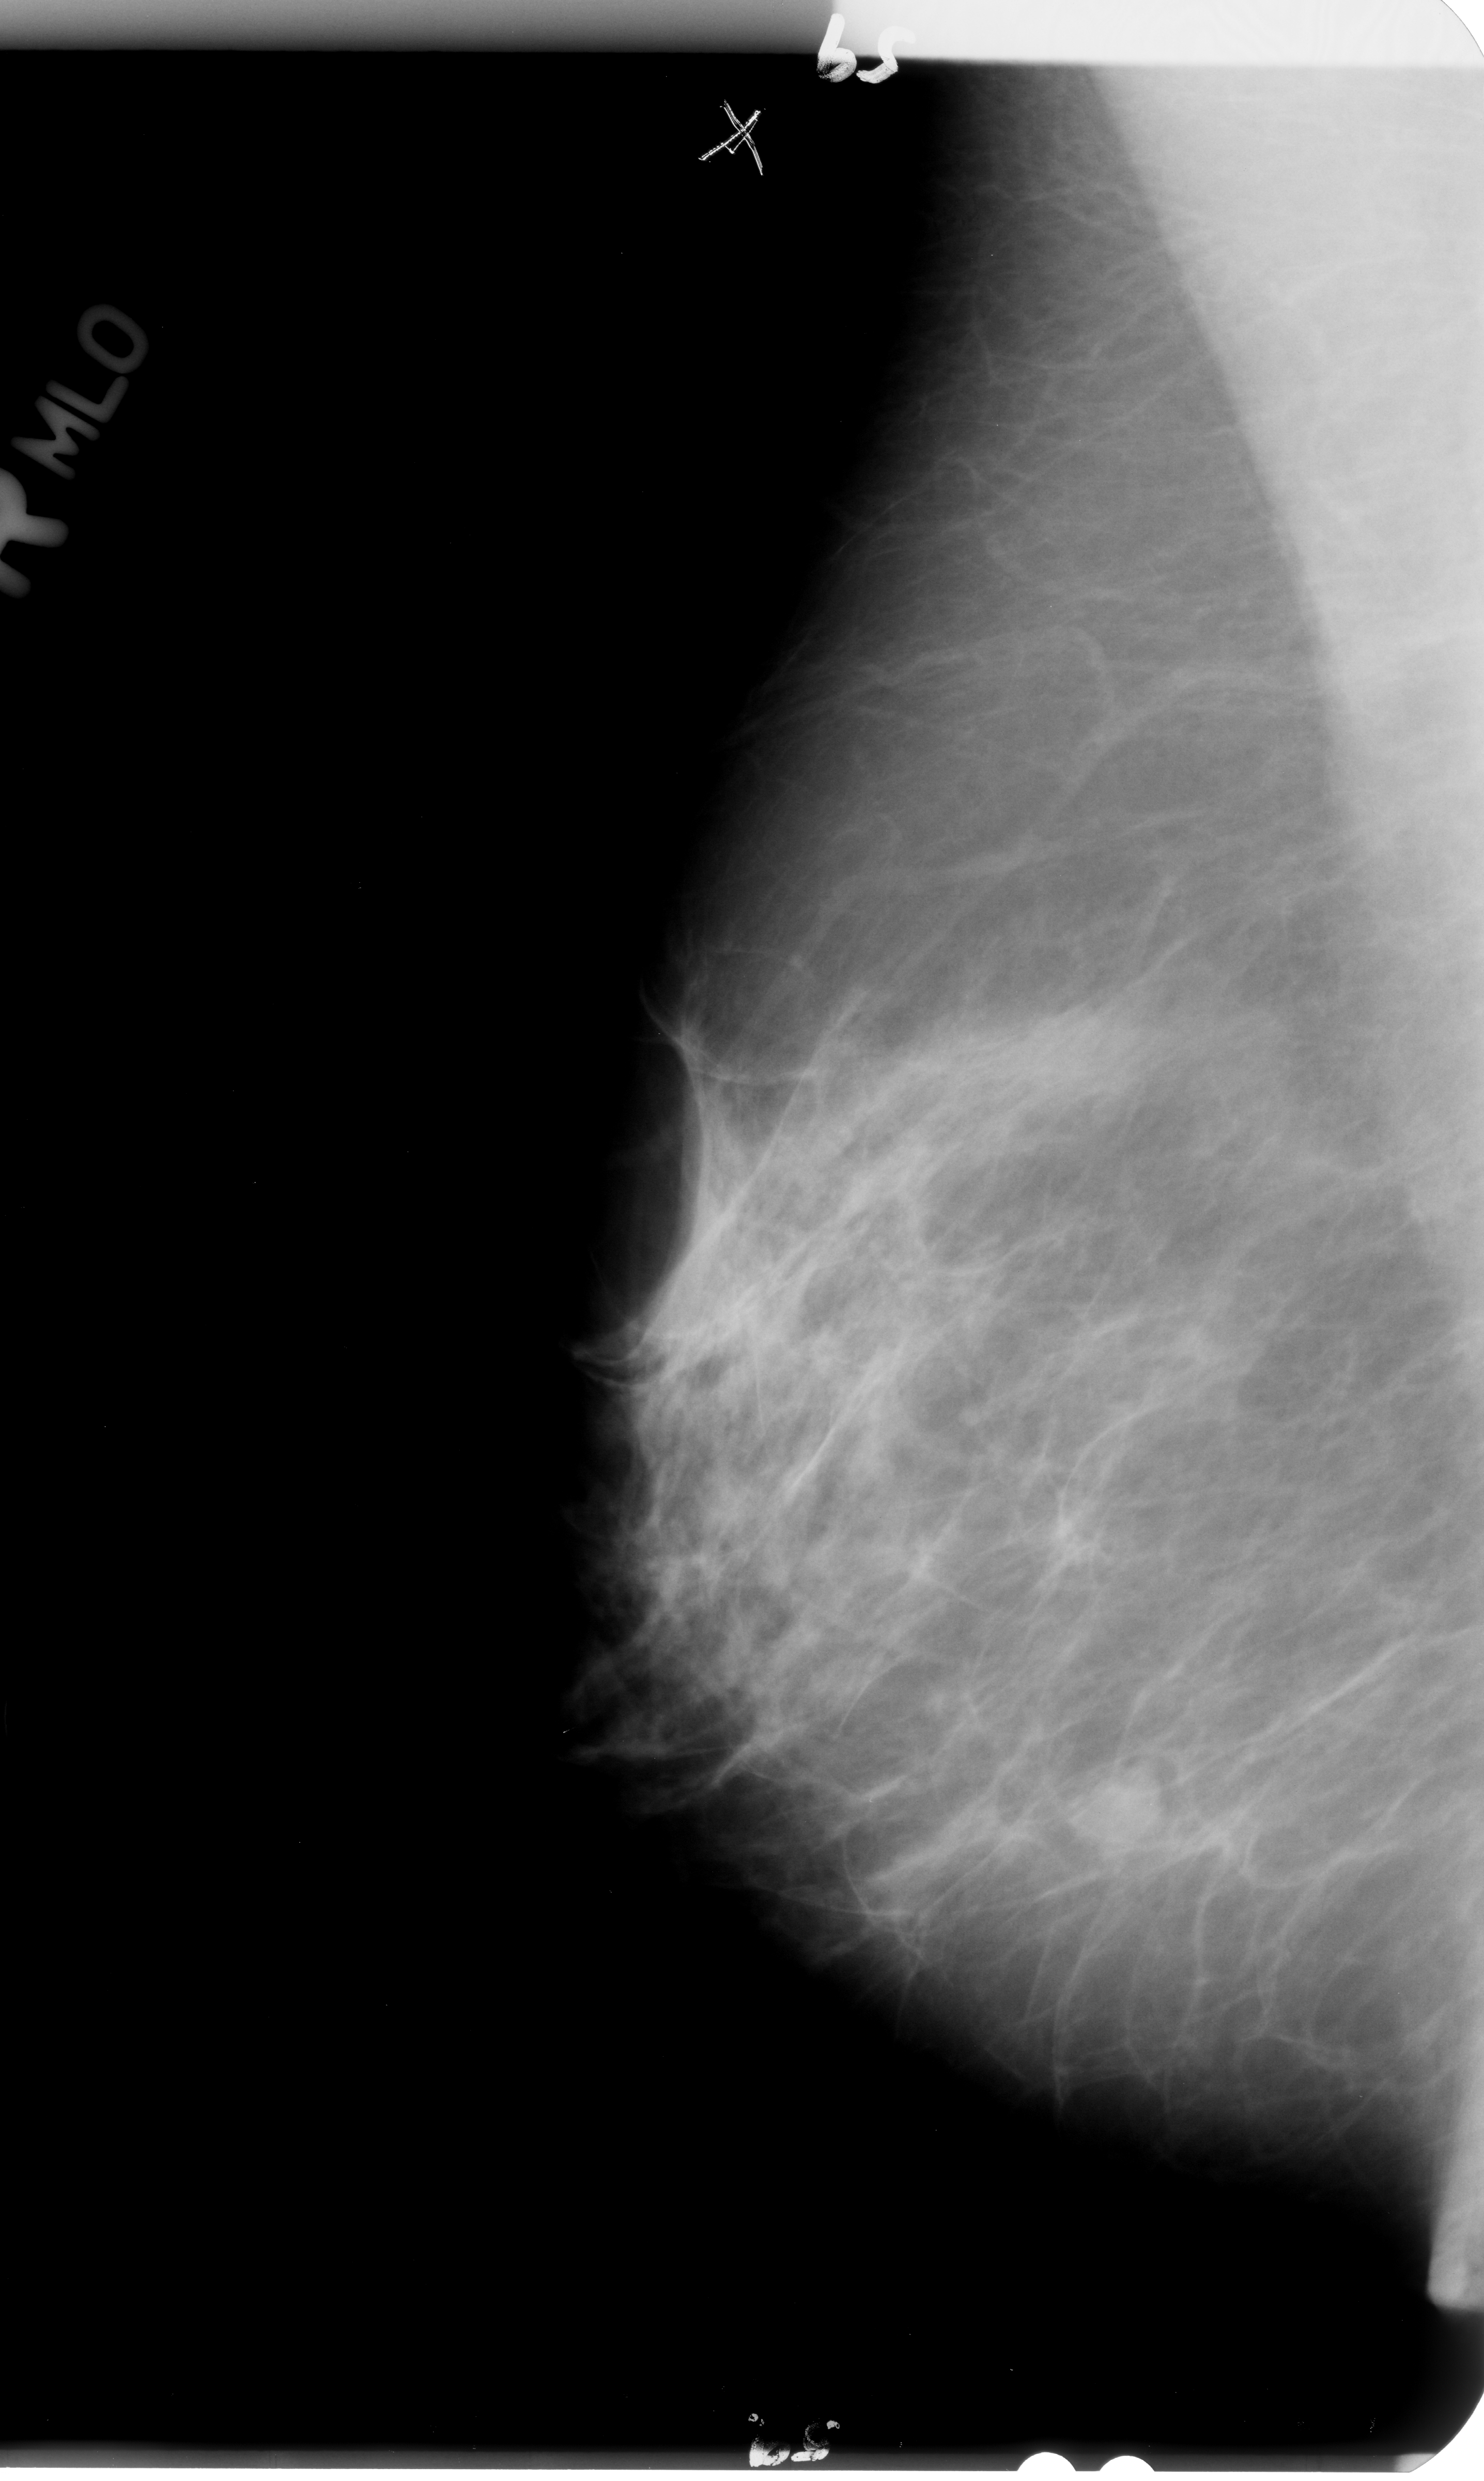
Mammogram (digitized film); right breast; mediolateral oblique (MLO) view; breast composition: scattered fibroglandular densities (BI-RADS density category 2 of 4).
- Abnormality record for this image: mass, shape irregular, margins microlobulated / ill defined; BI-RADS assessment category 4; pathology (as recorded): benign.